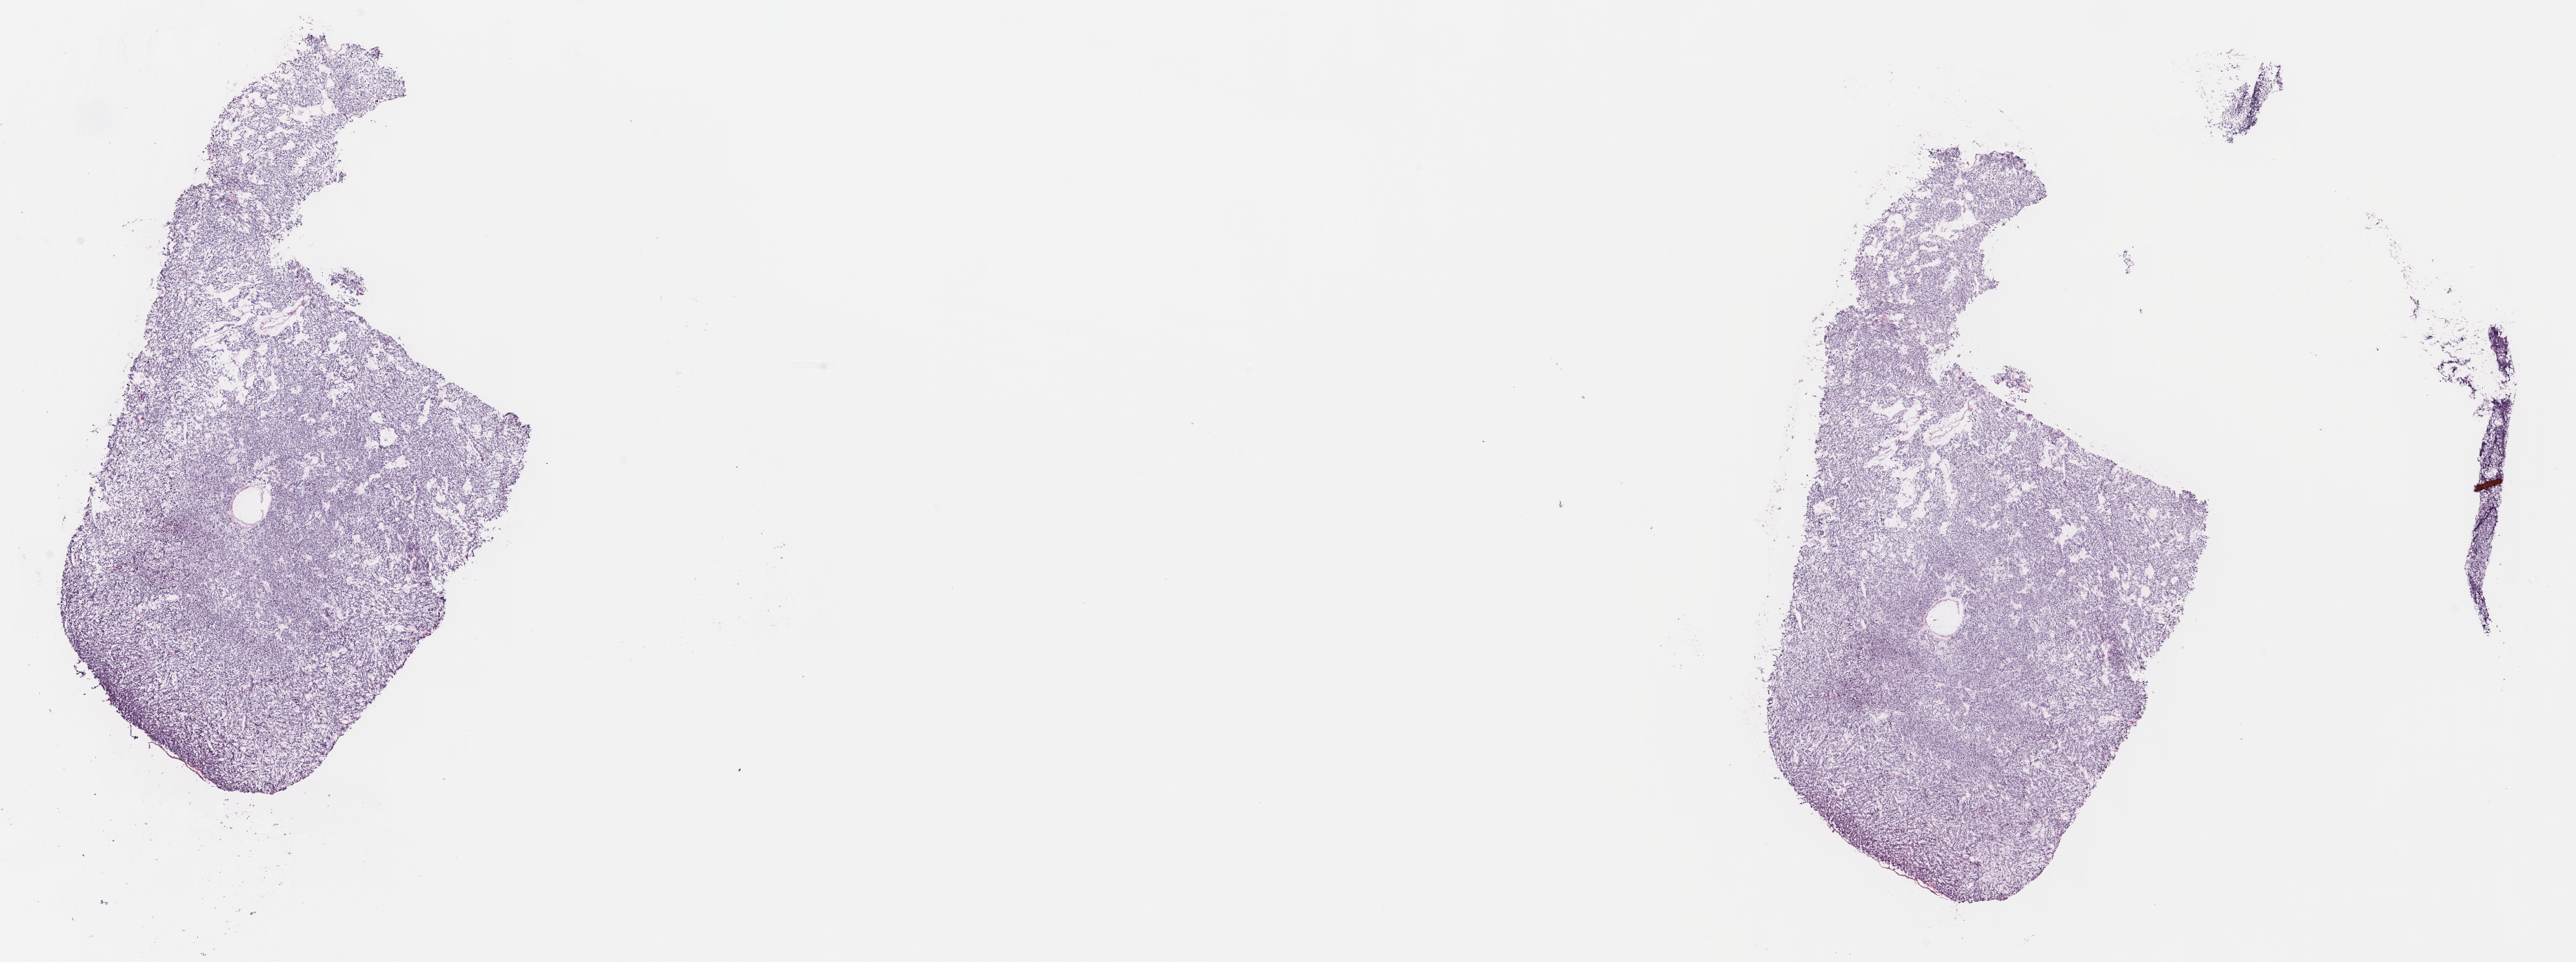
Whole-slide histology image, H&E — low-resolution overview of the scanned area, about 30.2 x 11.3 mm (slide scanned at 40x); frozen section from the top of the tissue portion; primary tumour sample from the retroperitoneum and peritoneum. Female, age 69 years at initial diagnosis.
Pathologic diagnosis: Extra-adrenal paraganglioma, NOS.